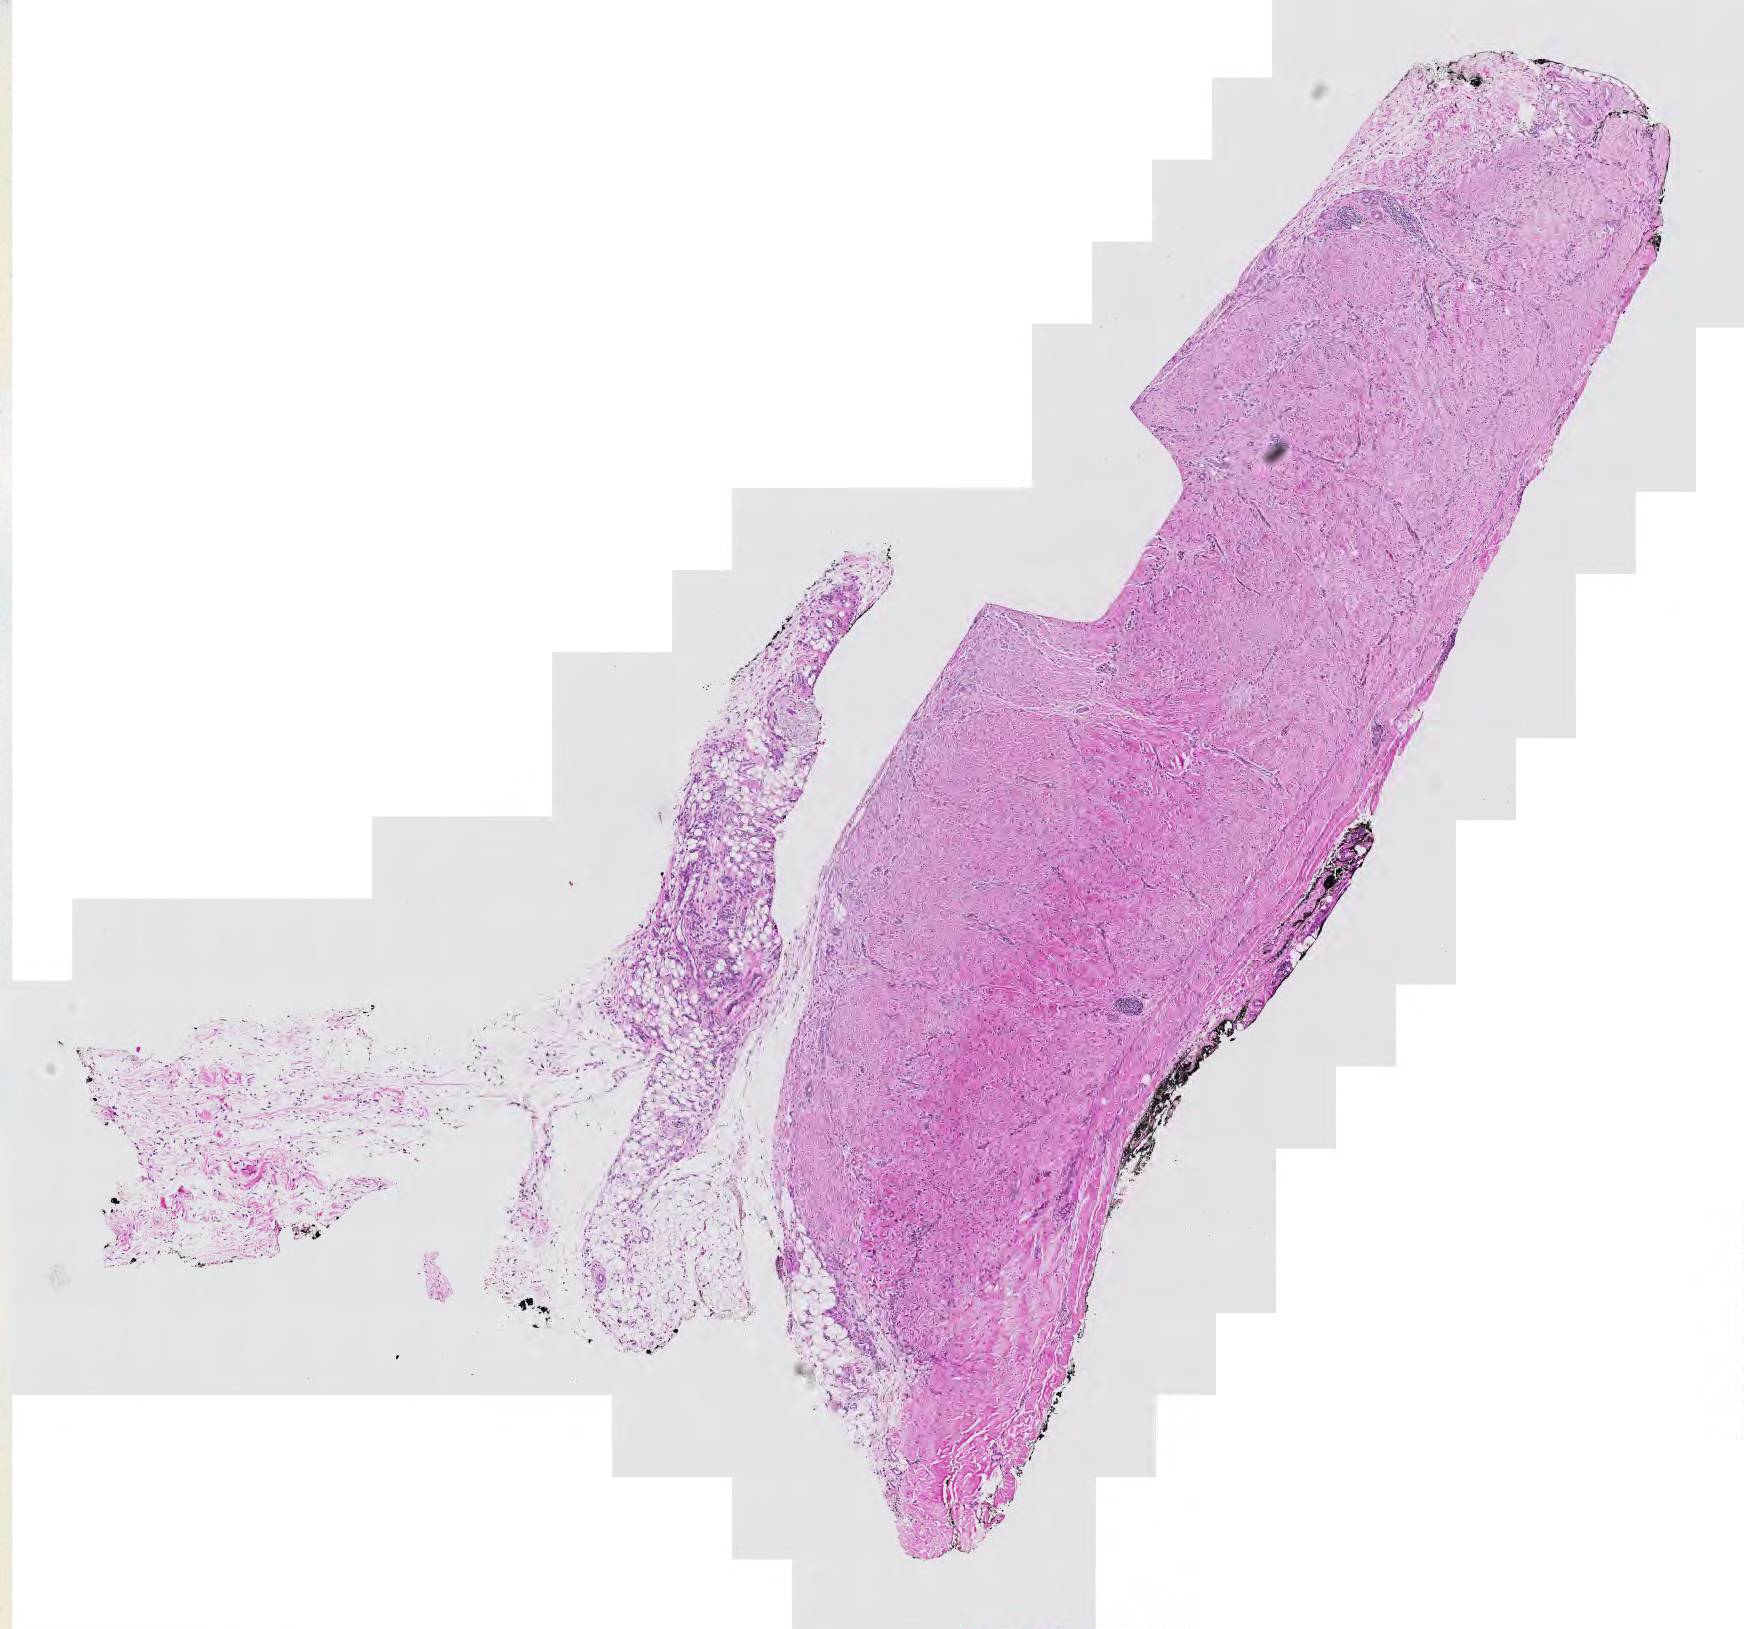
Digitized Hematoxylin and eosin (H&E) stained tissue section (whole slide), low-resolution overview of the scanned area, about 9.0 x 8.4 mm. Tumour tissue sample. 72-year-old female patient.
• patient diagnosis (cohort enrolment): sarcoma (site not recorded at cohort level)